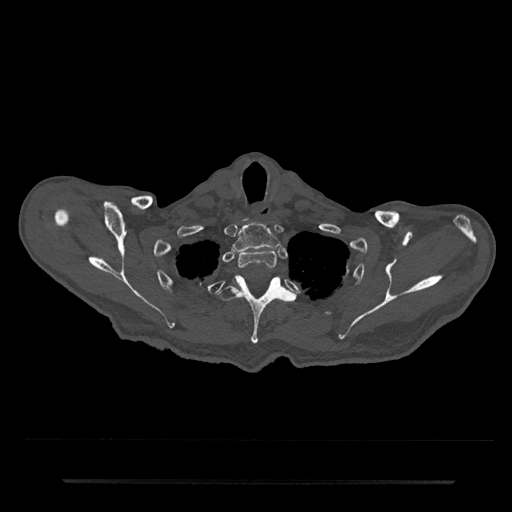
CT including the spine, one axial slice. Position 681 of 797 along the scan axis. 120 kVp. Bone window (W 1800 / L 400 HU). 0.5 mm slice thickness. 512 × 512 image matrix, field of view 427 × 427 mm. Patient: male, 74 years. From the clinical record (not read from this slice): primary cancer: prostate.
Outlined on this slice (semi-automatically segmented with operator editing):
- T1 vertebra: bounding box (x1, y1, x2, y2) in pixels: (232, 223, 280, 252)
- T2 vertebra: (238, 250, 277, 269)
- T3 vertebra: (217, 275, 295, 344)